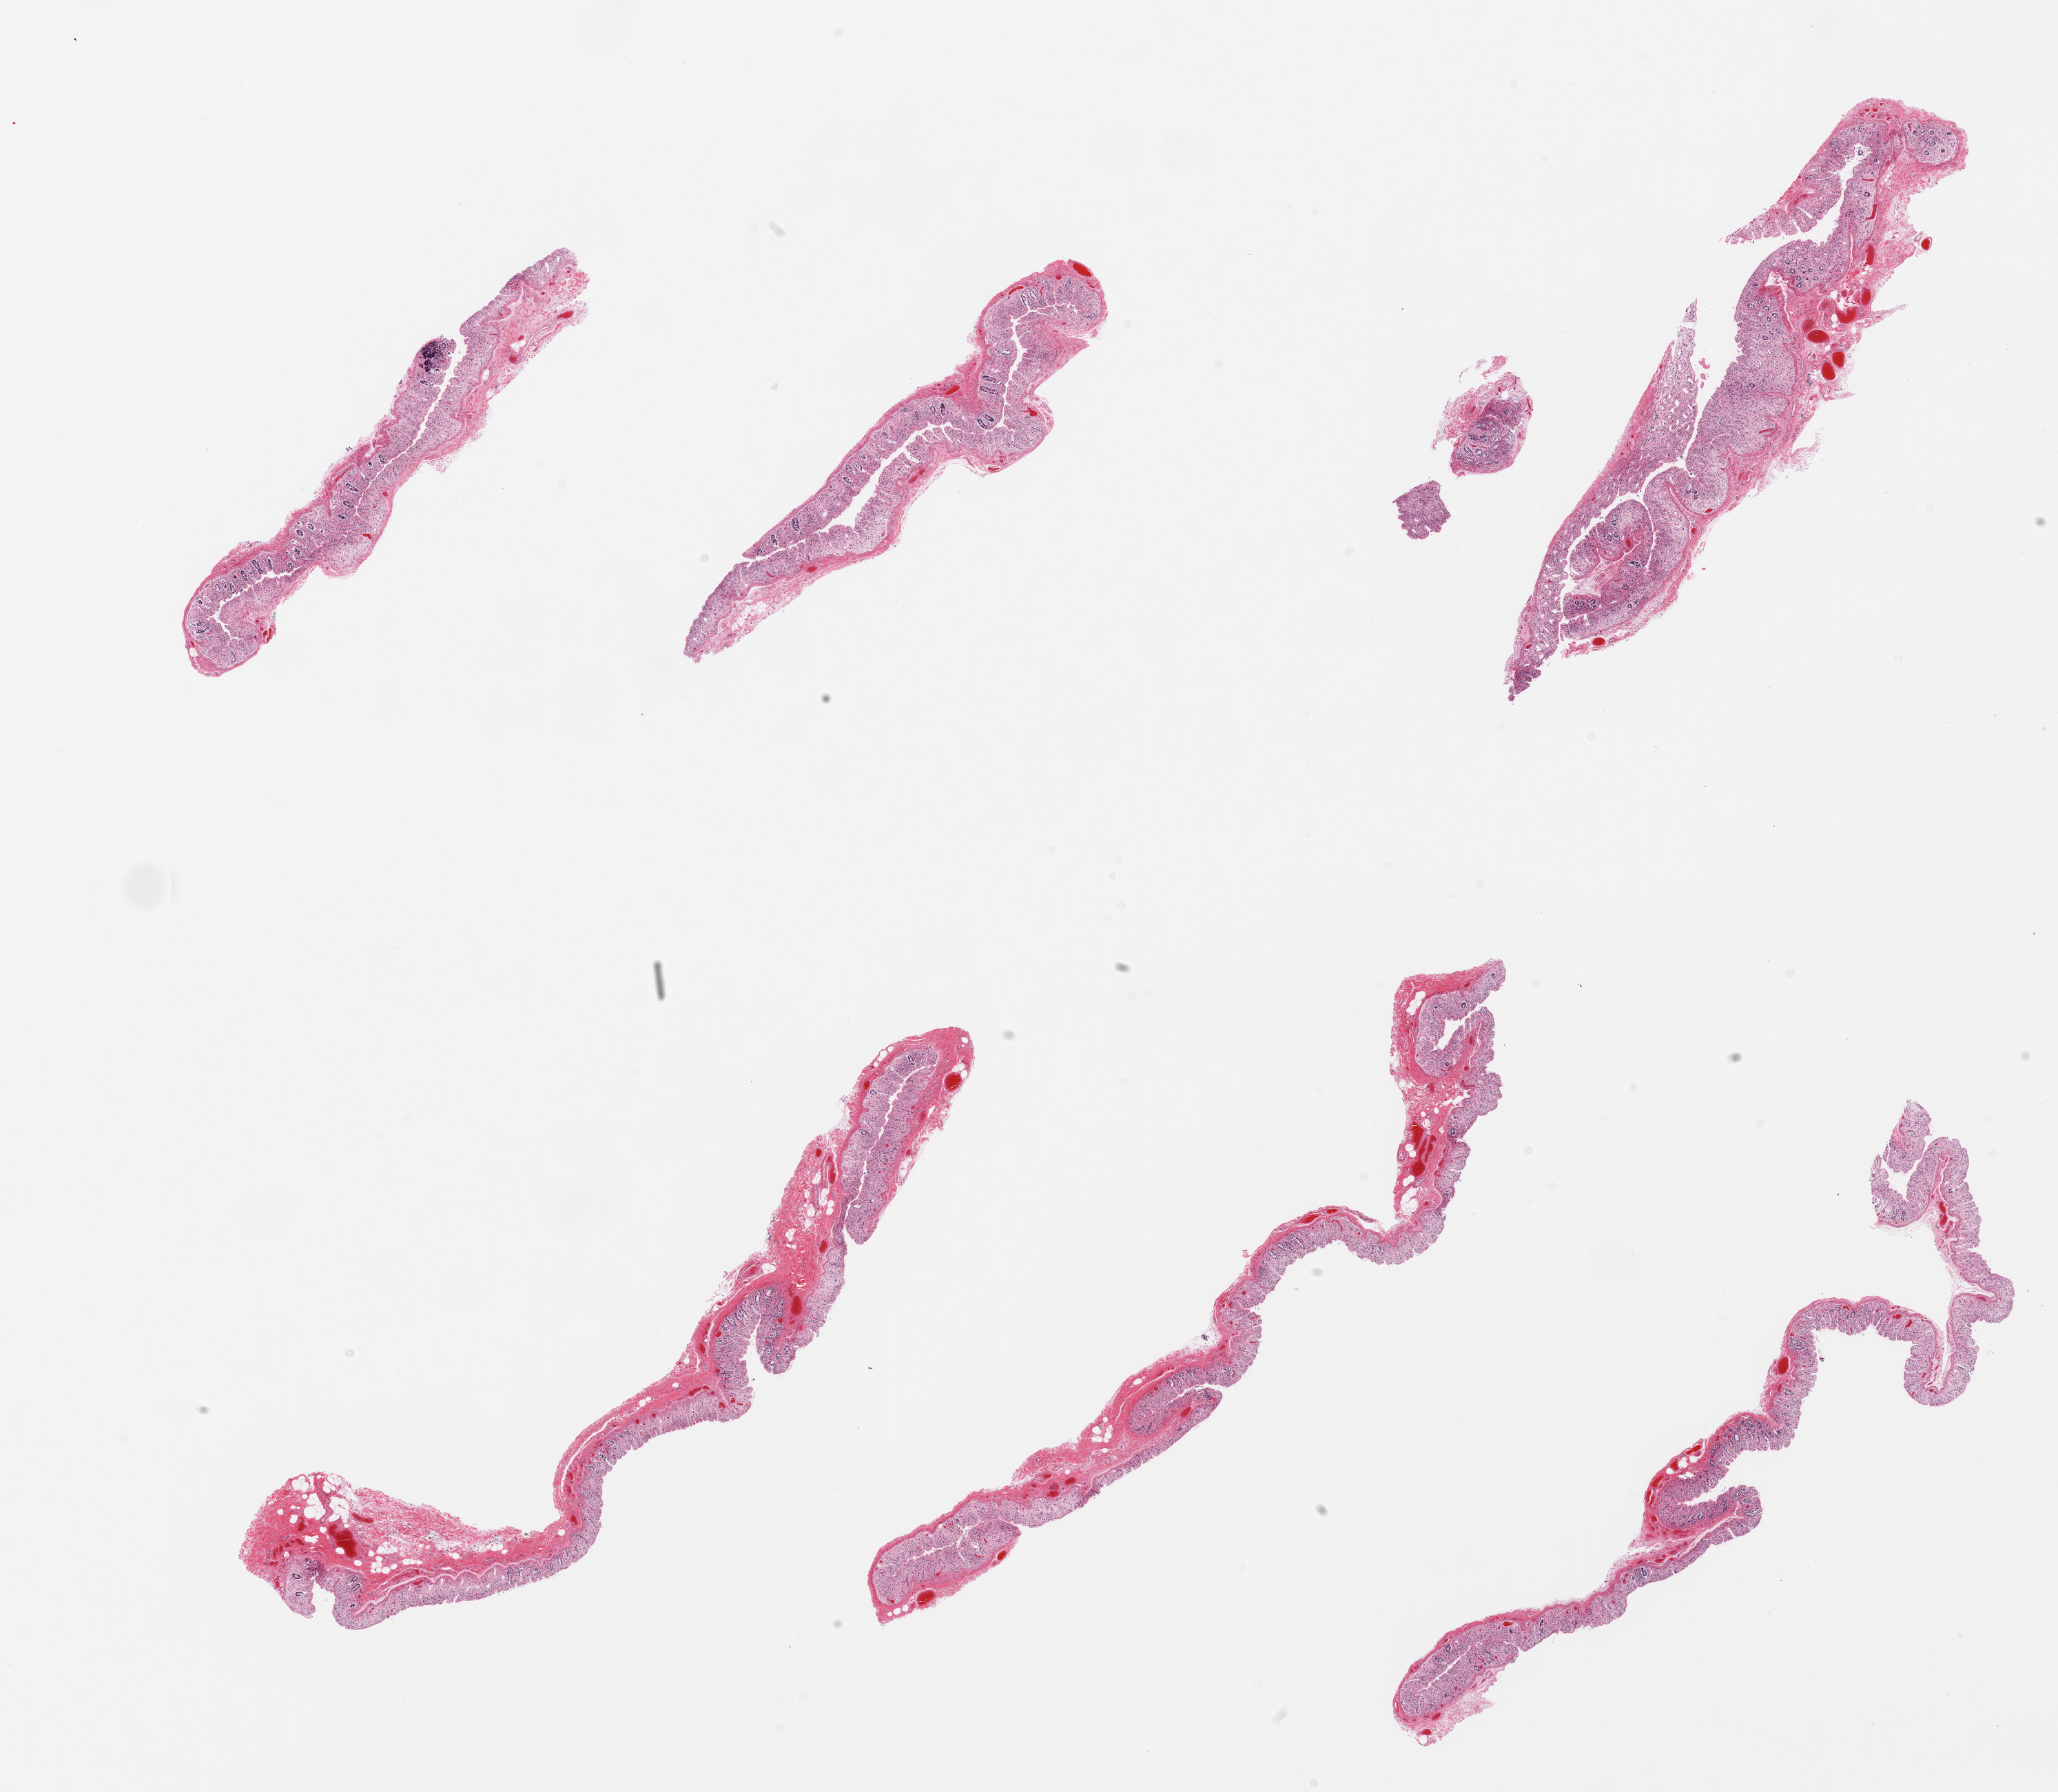
Digitized H&E-stained section — low-resolution overview of the scanned area, about 23.6 x 20.6 mm, PAXgene-fixed paraffin-embedded (PFPE) section, sampled site (target tissue): transverse colon, donor tissue sample.
• pathologist's review note for this sample: 6 pieces, mucosa totaly autlyzed